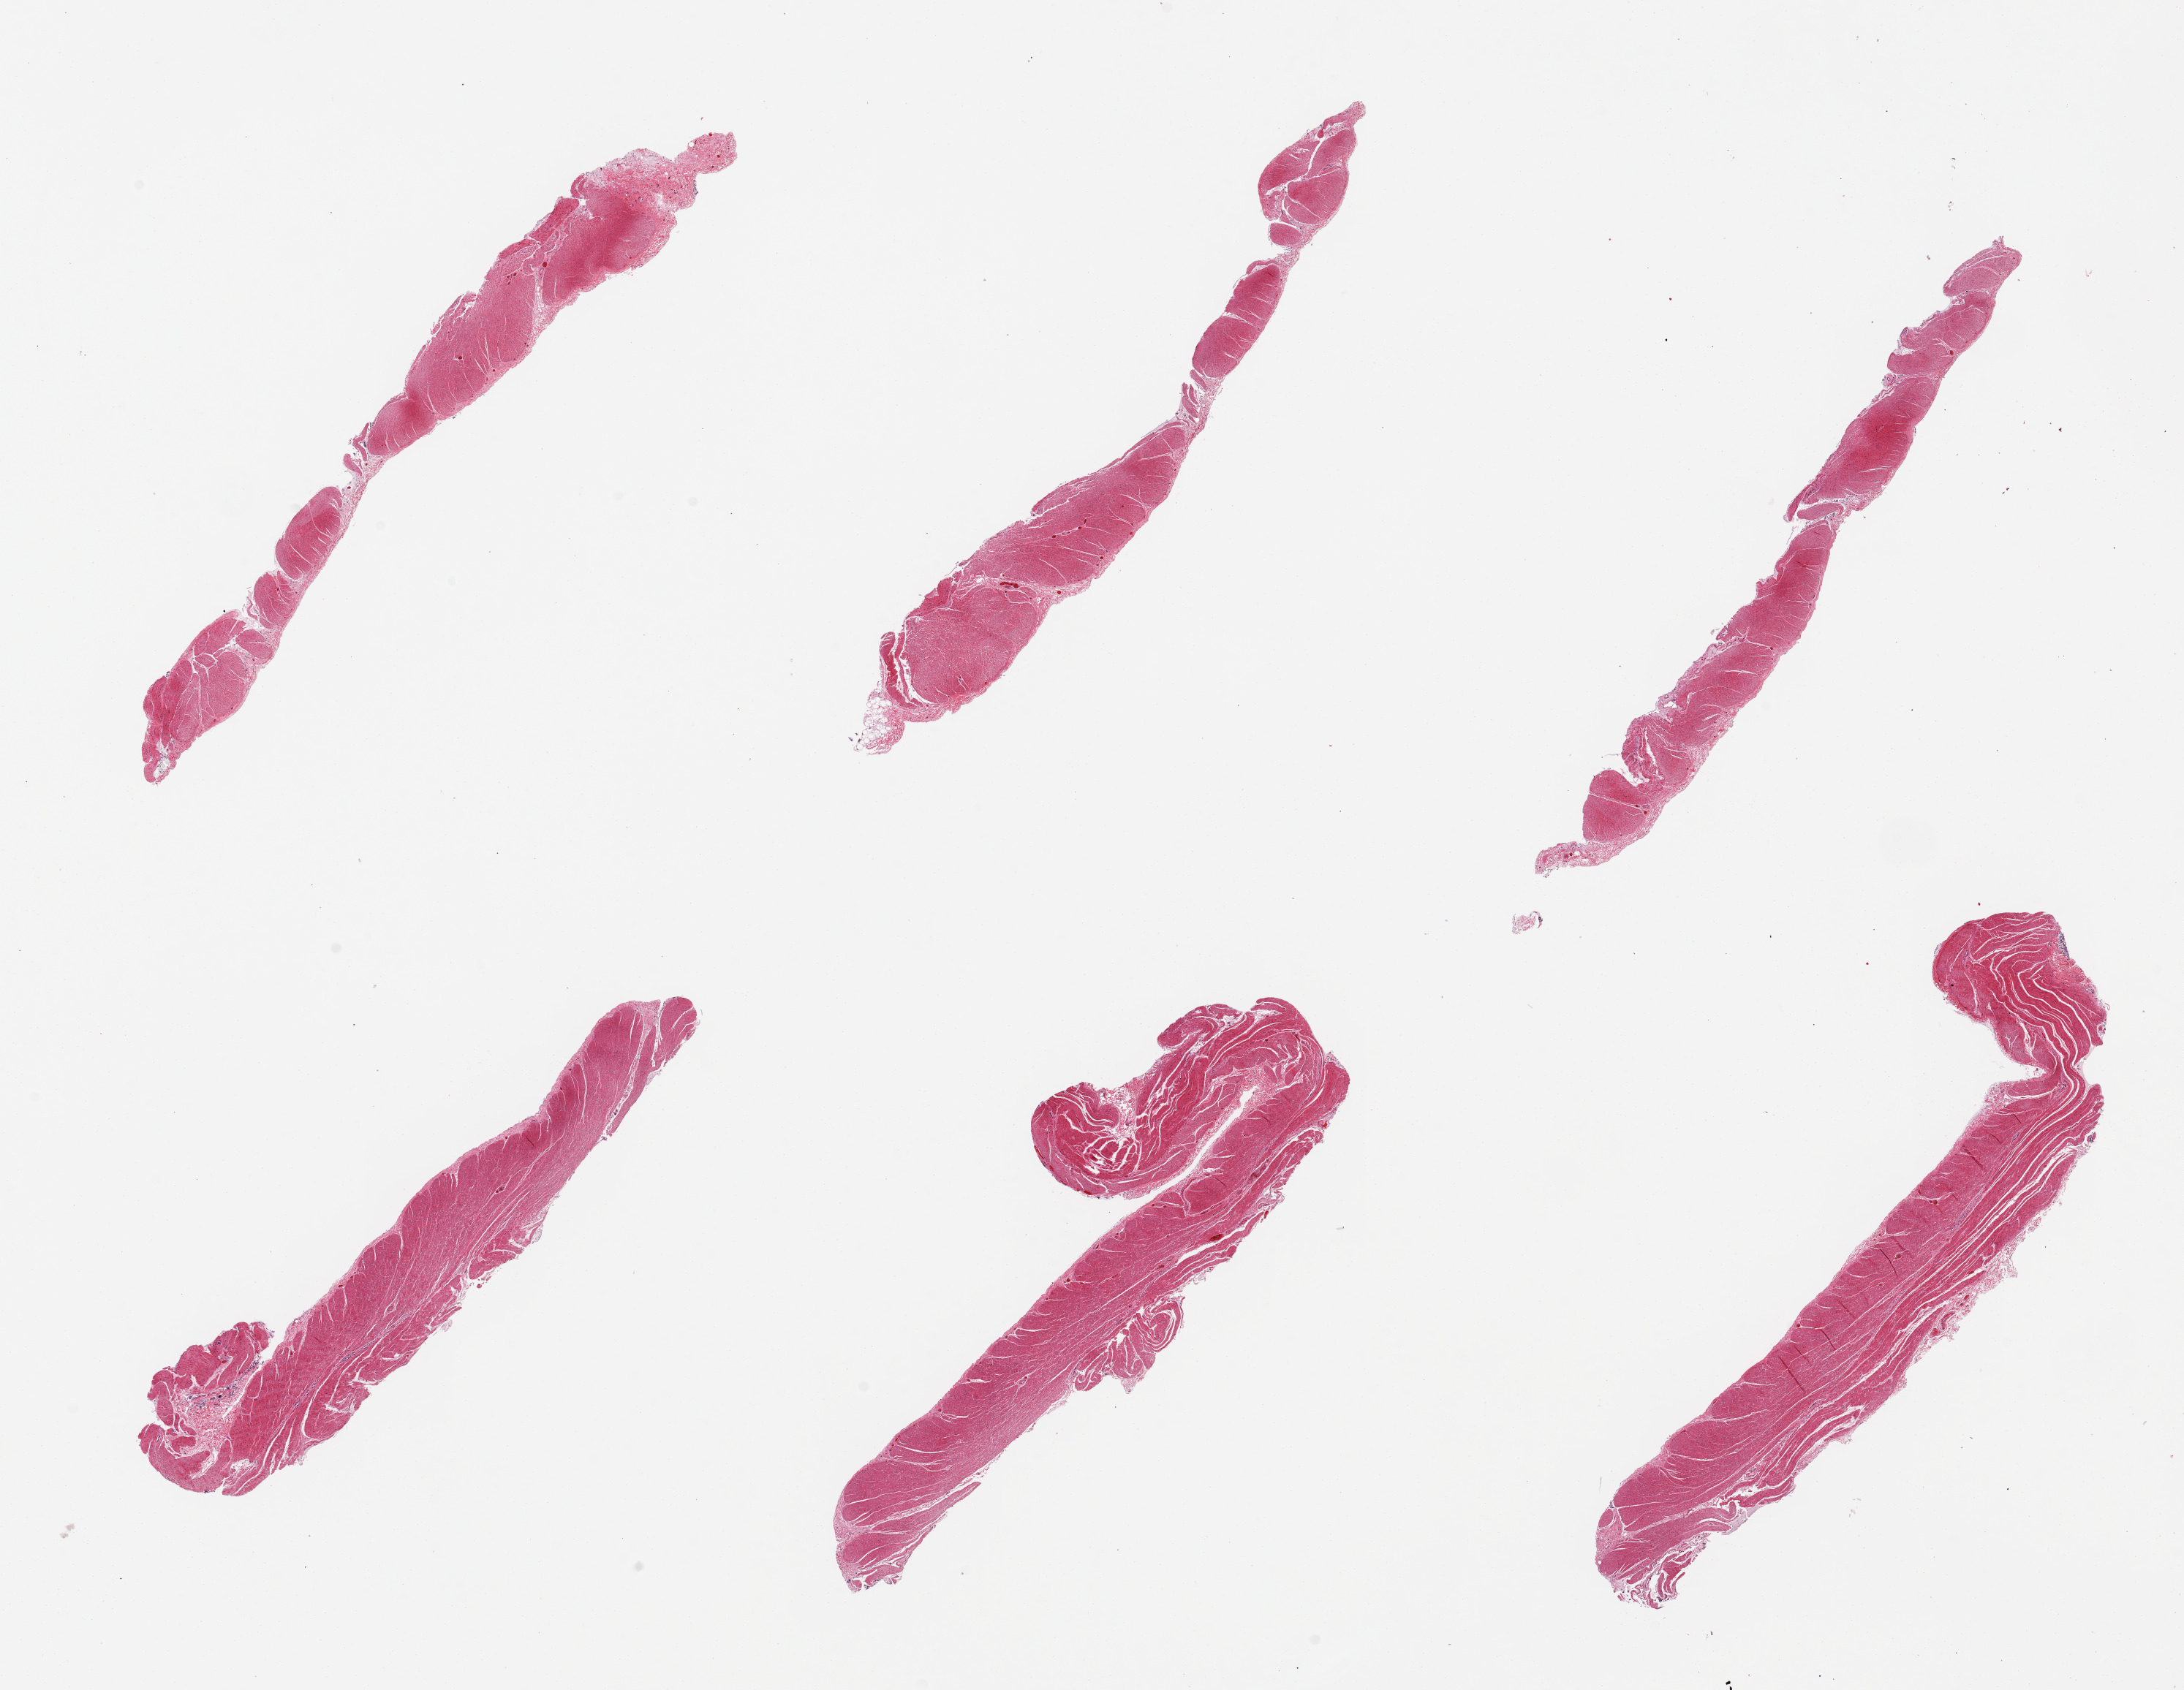
Hematoxylin and eosin (H&E) whole-slide image, brightfield — low-resolution overview of the scanned area, about 23.6 x 18.3 mm (acquisition: 20x scan). PAXgene-fixed, paraffin-embedded tissue. Target tissue: sigmoid colon. Tissue donor sample. Male donor.
Review note (as recorded): 6 pieces; well trimmed.